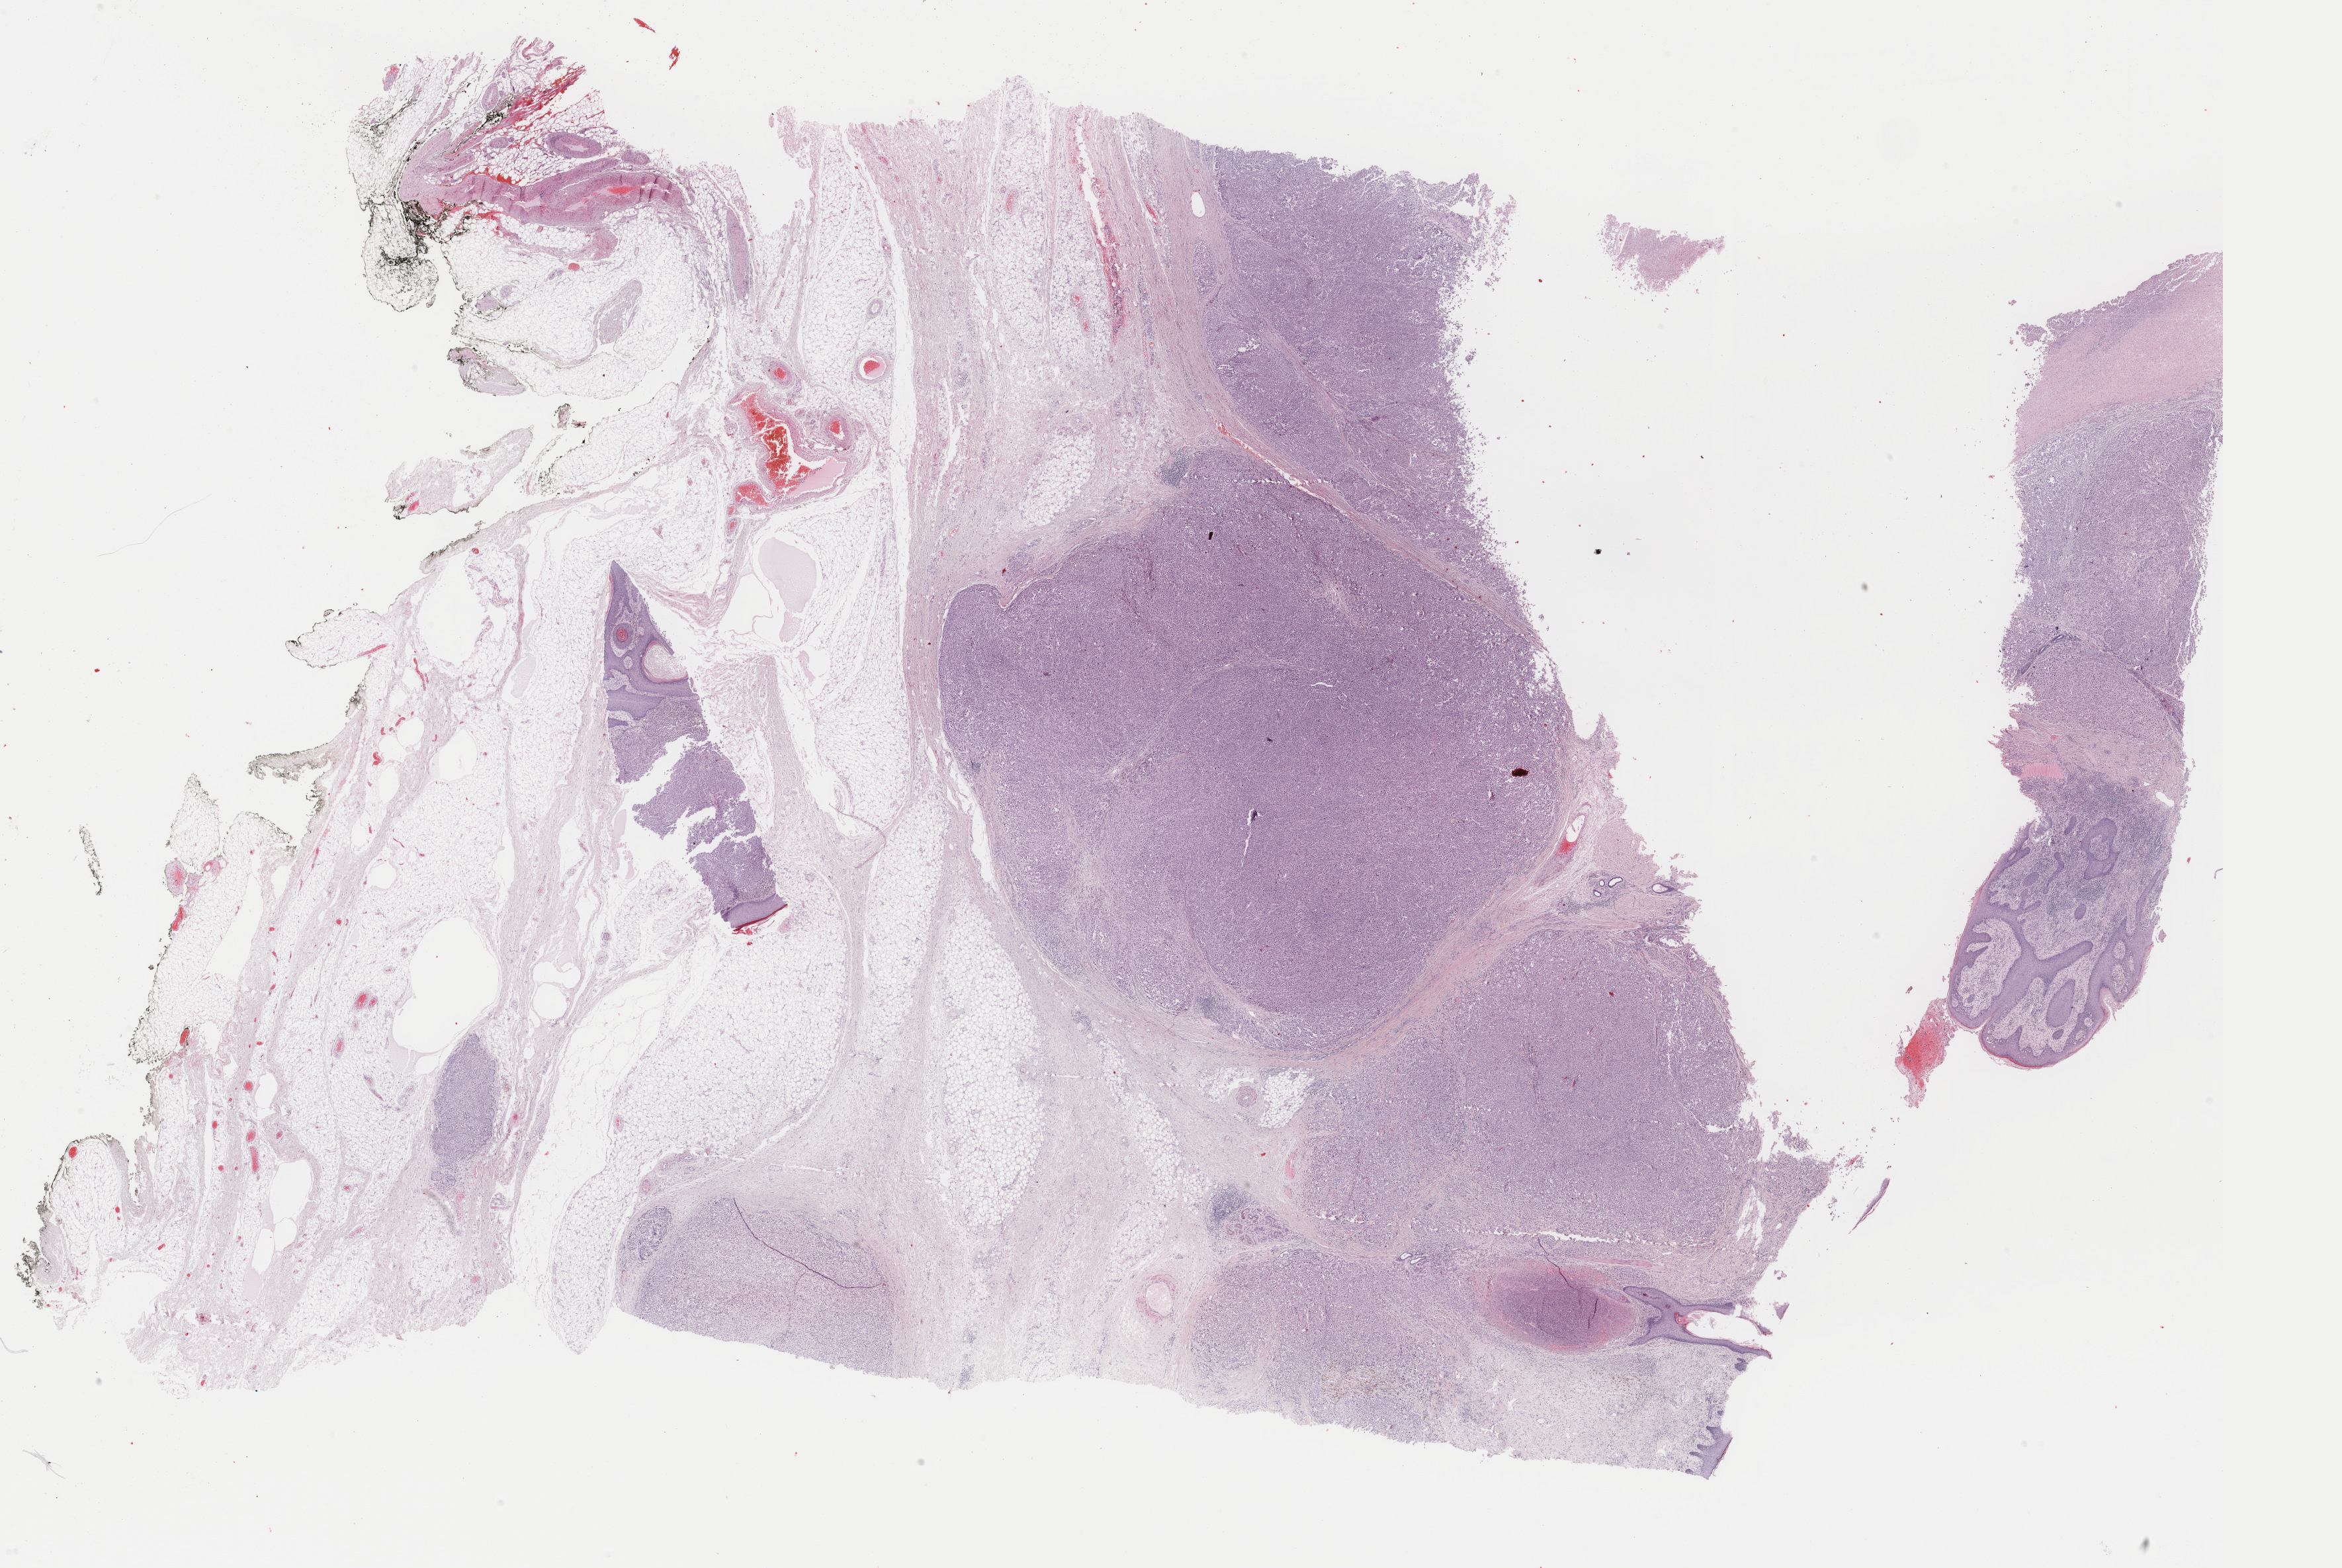
Hematoxylin and eosin (H&E) stained whole-slide image — shown as a low-resolution overview of the whole scanned area (about 28.1 x 18.8 mm), FFPE section, sample: primary tumour, skin. Patient: male, age at initial diagnosis 50 years.
* histologic diagnosis: Nodular melanoma